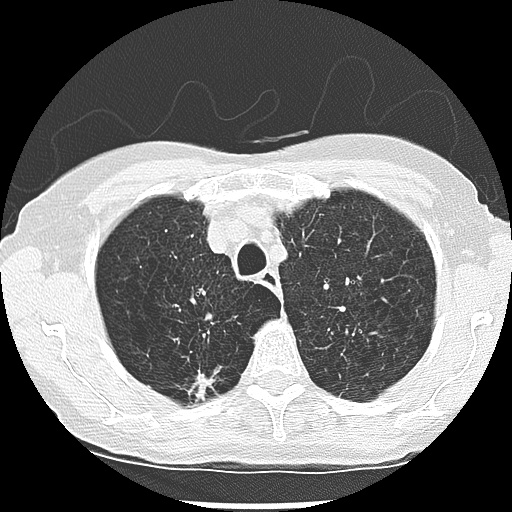
Low-dose screening chest CT, one axial slice. Position 219 of 265 along the scan axis. Reconstruction kernel LUNG. Lung window (W 1500 / L -600 HU). 512 × 512 image matrix, field of view 300 × 300 mm.
Structures marked on this image (outlined manually by an expert reader):
- lesion 1 (nodule, upper lobe of right lung): bounding box [x1, y1, x2, y2] px = [195, 373, 215, 400]